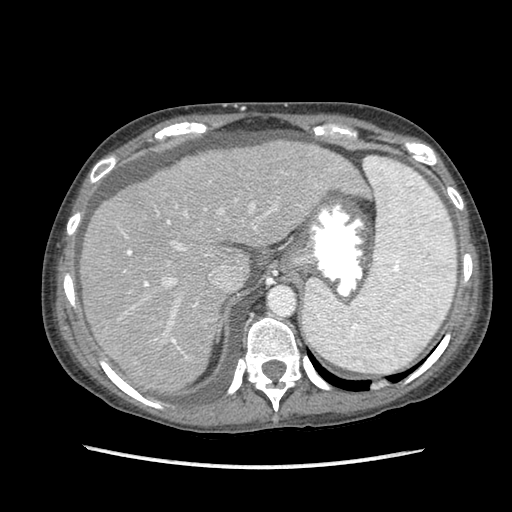
Contrast-enhanced abdominal CT (liver protocol), one axial slice. Slice 66 of 87 in the series (ordered by position). Reconstruction kernel STANDARD. 120 kVp. Soft-tissue window (W 400 / L 40 HU). 2.5 mm slice thickness. 512 × 512 image matrix, field of view 340 × 340 mm. Case-level facts recorded for this patient, not image findings: diagnosis: hepatocellular carcinoma (patient treated with transarterial chemoembolisation; whether this scan precedes or follows treatment is not stated here); TNM stage (as recorded): Stage-IIIB; Child-Pugh class: A; tumour differentiation: no biopsy; tumour nodularity: uninodular.
Structures marked on this image (semi-automatic segmentation, software-assisted and operator-edited):
- abdominal aorta: bounding box <269,287,294,315> (left, top, right, bottom; pixels)
- liver parenchyma outside the tumour (the mass and vessels are separate outlines, so this box may not span the whole liver): <80,140,366,392>
- liver vessels: <118,167,341,359>